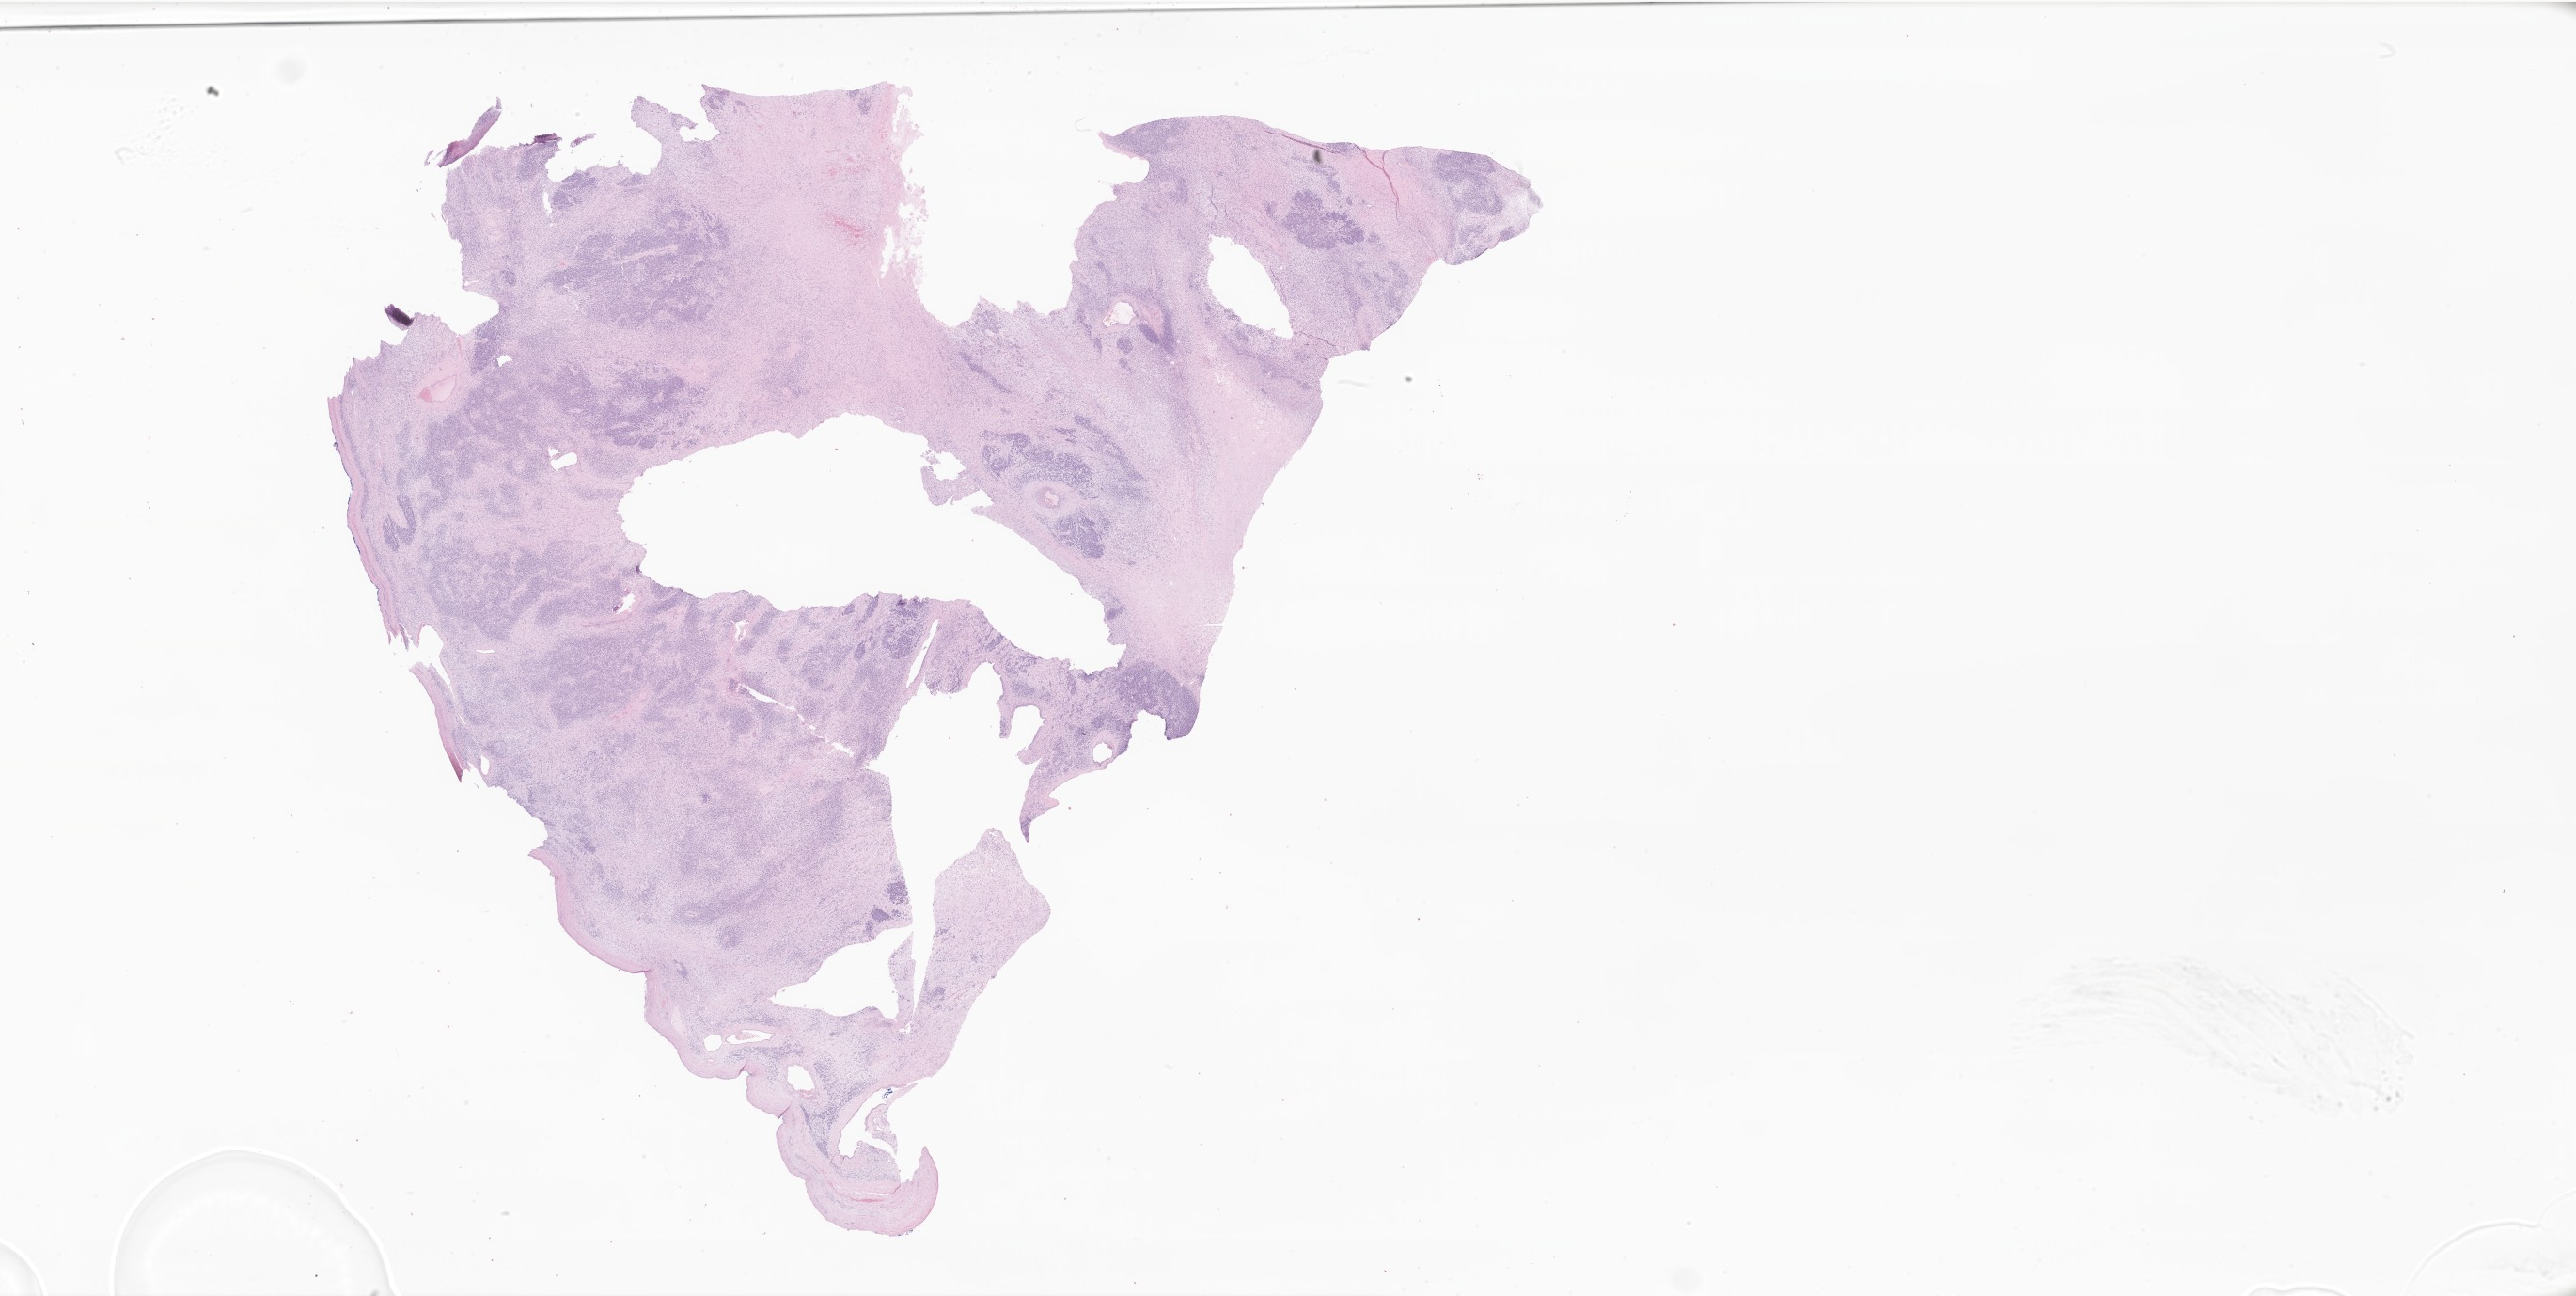
Whole-slide image, hematoxylin and eosin (H&E) stain of tumor tissue from the testis, shown as a low-resolution overview of the whole scanned area (about 46.2 x 23.2 mm), formalin-fixed, paraffin-embedded (FFPE) tissue. Patient: male, age 157 months (13 years 1 month).
• recorded diagnosis: Alveolar rhabdomyosarcoma